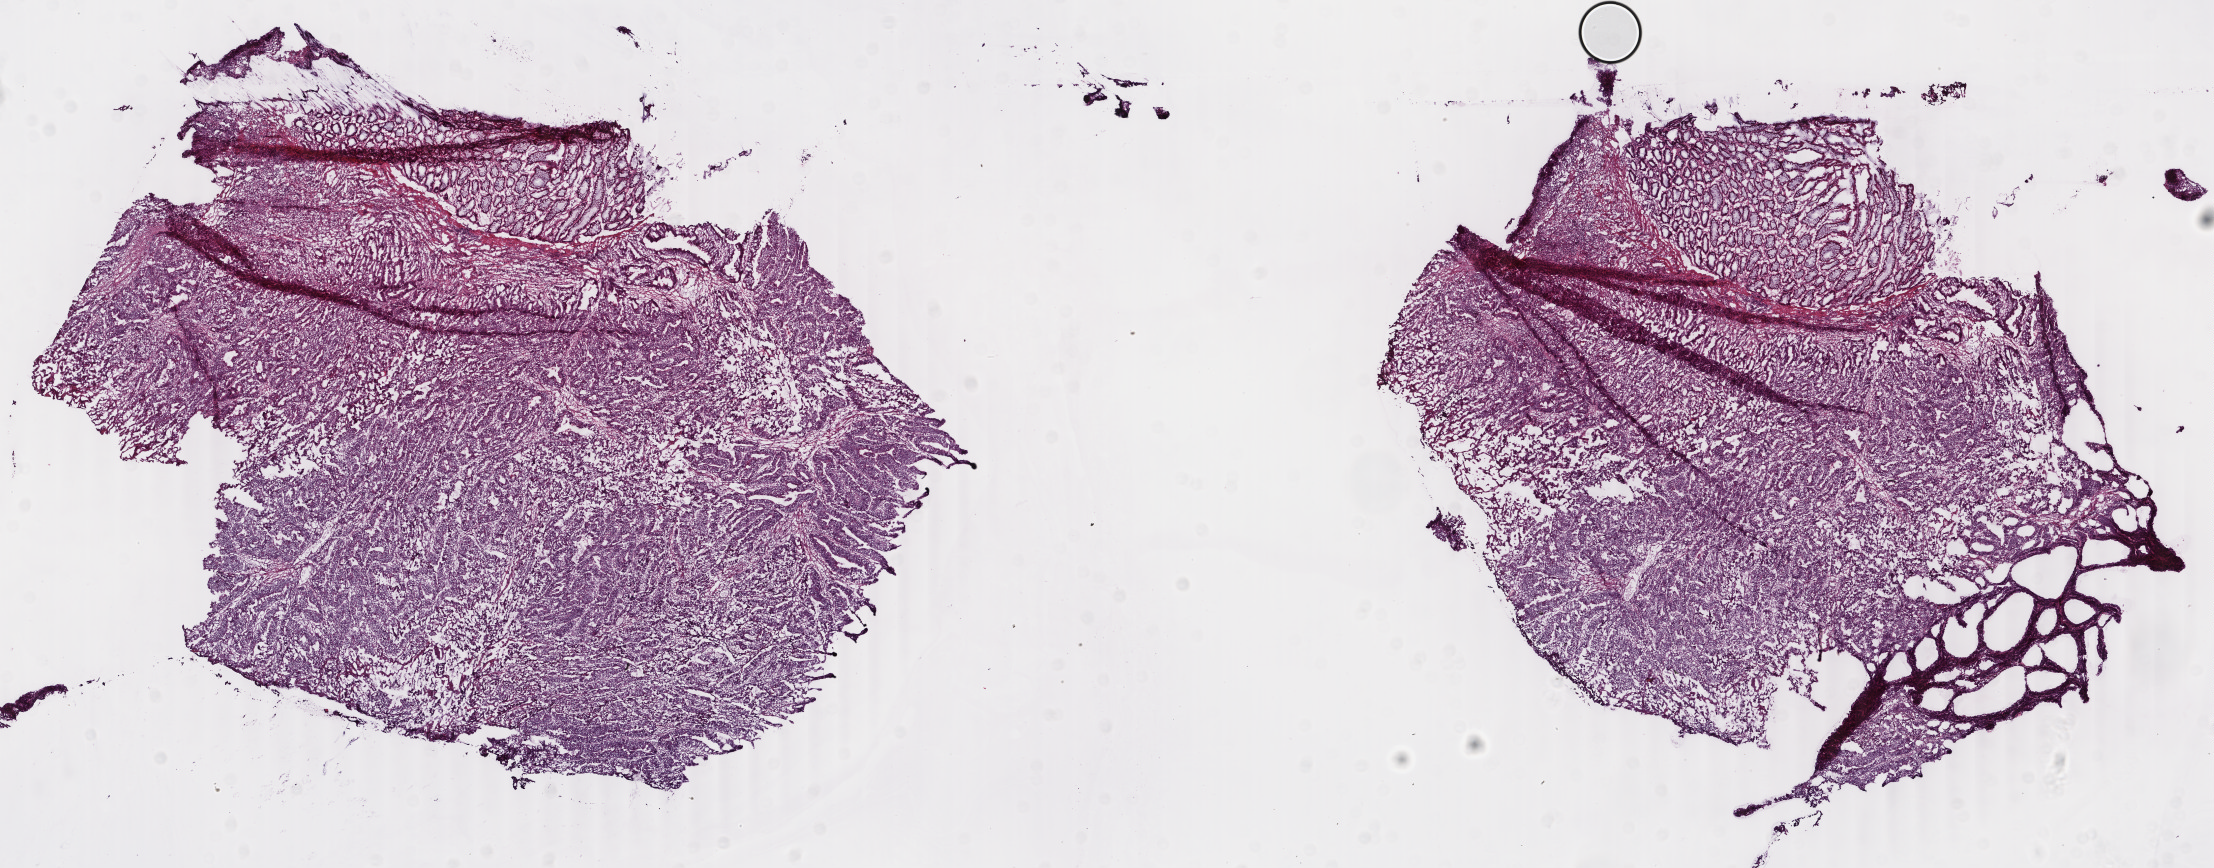
Hematoxylin and eosin (H&E) stained whole-slide image, a low-resolution overview of the entire scanned area, about 17.6 x 6.9 mm (slide scanned at 40x), frozen section, primary tumour sample from the rectum. Female patient; age at initial diagnosis 67 years. Slide review estimates, as recorded: tumour cells 90%, tumour nuclei 85%, normal cells 6%, stromal cells 3%, necrosis 1%. Inflammatory infiltration, as recorded: lymphocyte infiltration 6%, monocyte infiltration 1%, neutrophil infiltration 2%.
Diagnosis: Adenocarcinoma, NOS. Lymph nodes positive (case pathology): 0 of 20 examined. AJCC pathologic stage: II (5th edition).